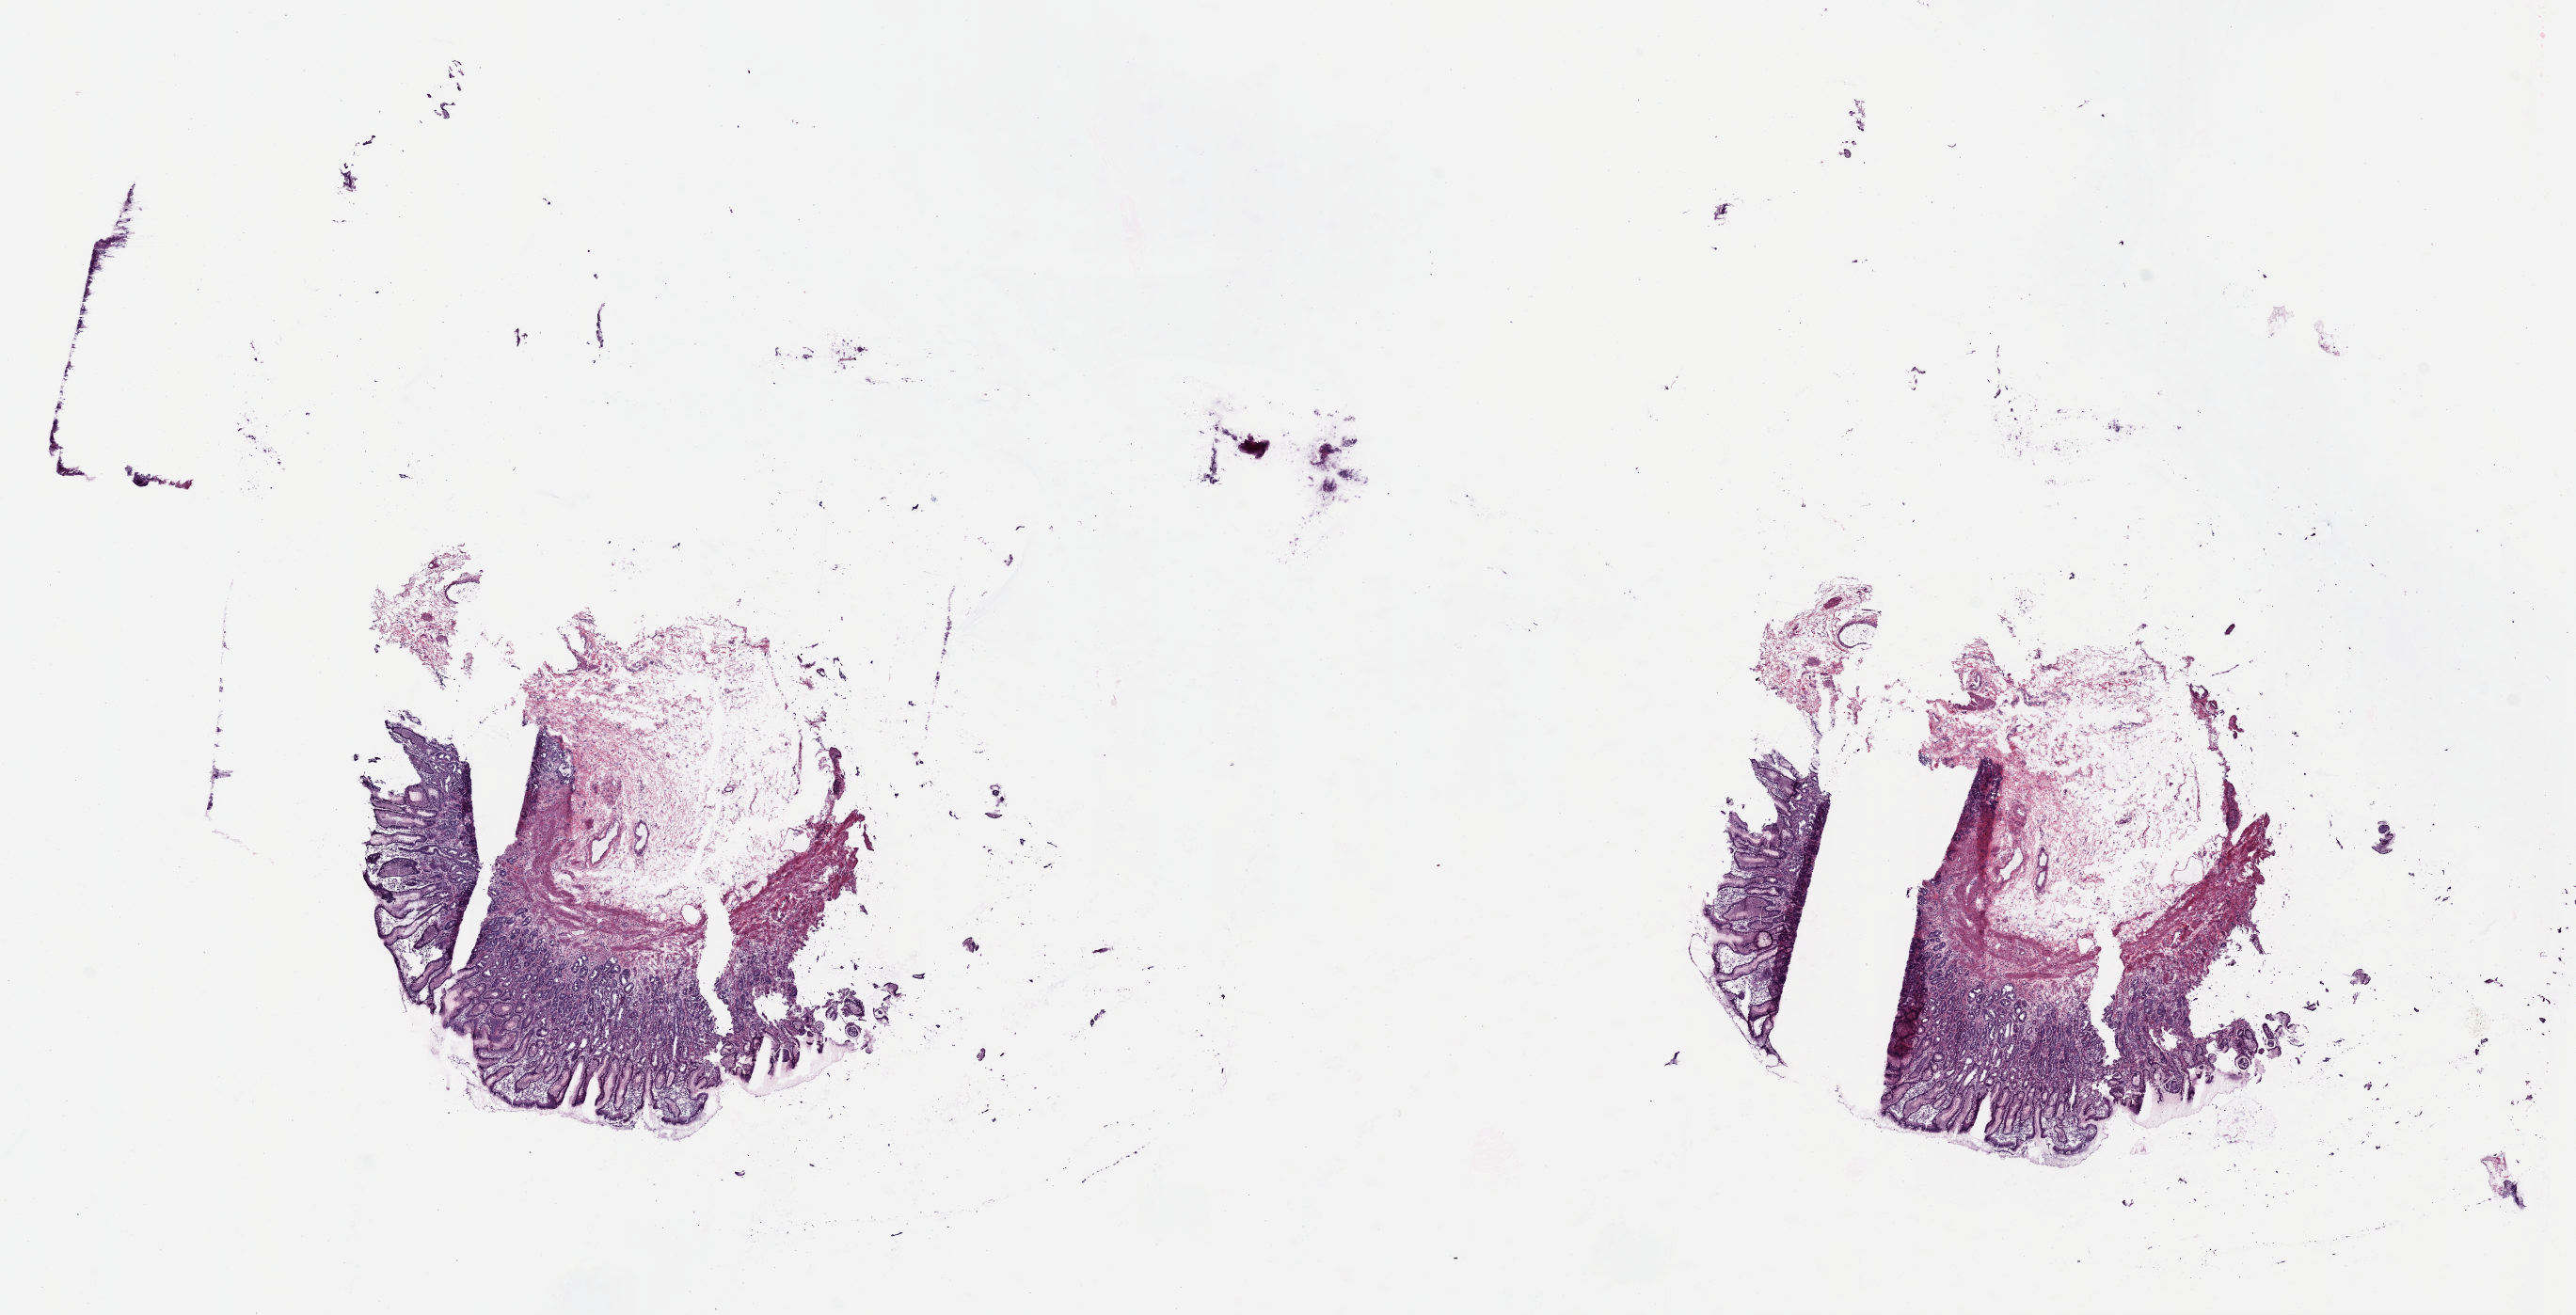
Digitized H&E tissue section (whole slide) — a low-resolution overview of the entire scanned area, about 21.6 x 11.0 mm (from a 20x scan); frozen section from the top of the tissue portion; esophagus, solid tissue normal (non-tumour tissue) sample. Female patient; age at initial diagnosis 79 years. Pathologist review of this section (percent, as recorded): tumour cells 0%, tumour nuclei 0%, normal cells 50%, stromal cells 50%, necrosis 0%. Infiltration values recorded for this section: lymphocyte infiltration 10%, monocyte infiltration 0%, neutrophil infiltration 0%.
This section: solid tissue normal (non-tumour) sample from the same patient. Patient diagnosis: Adenocarcinoma, NOS (lower third of esophagus).